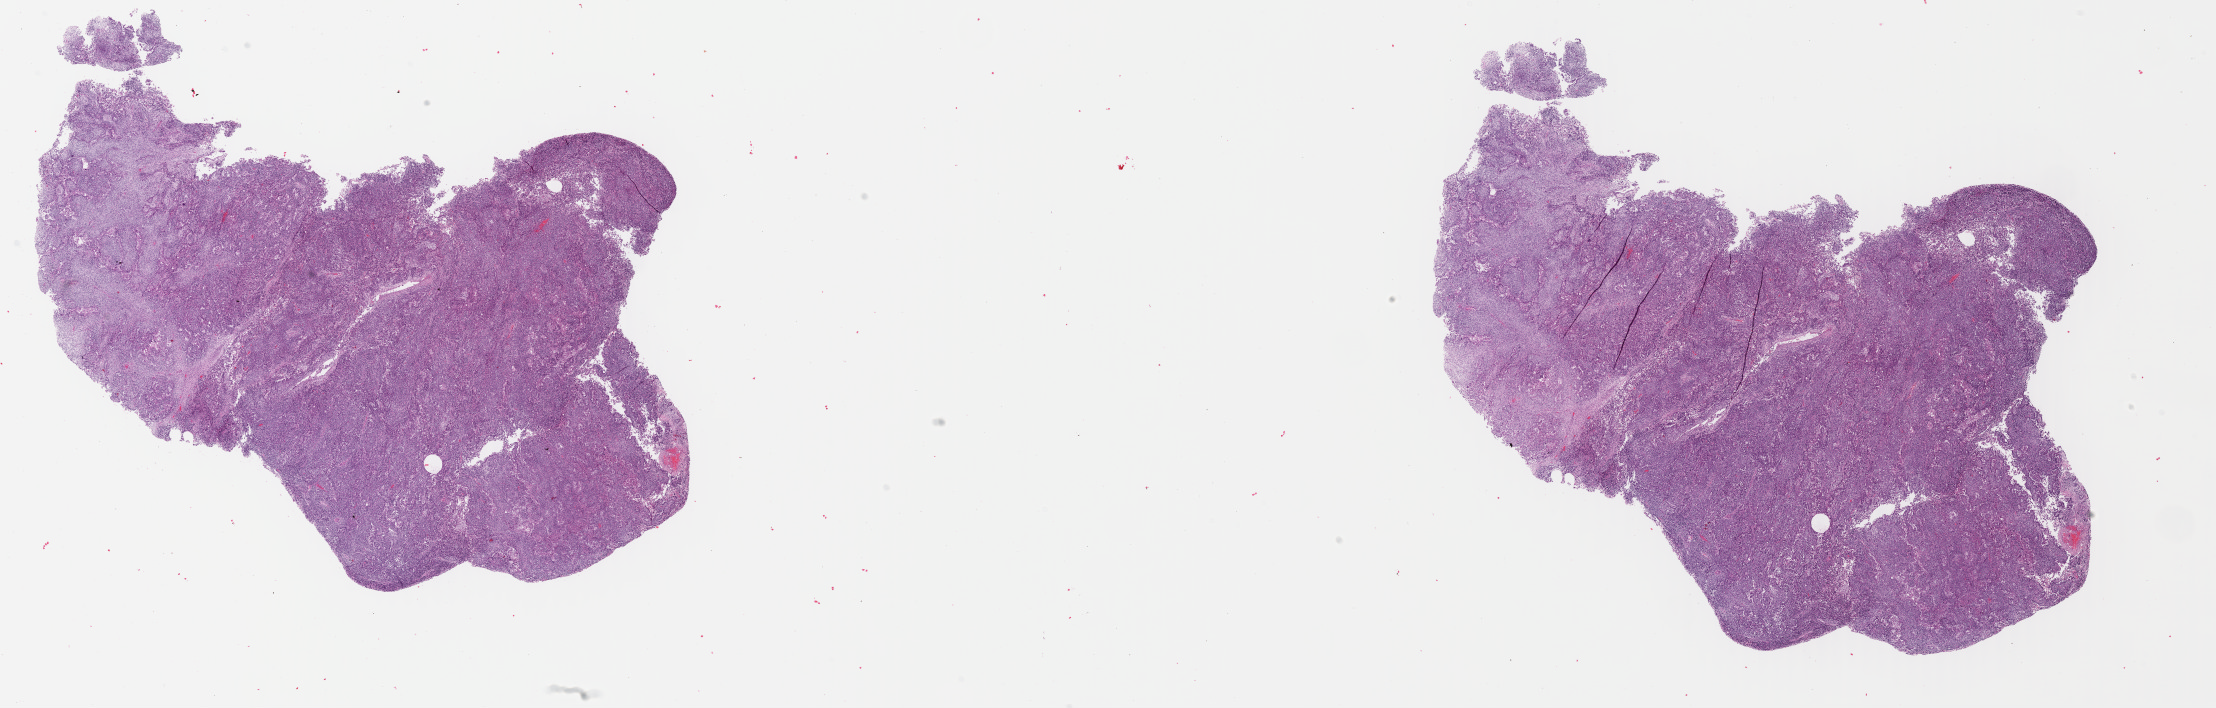
Digitized H&E-stained tissue section (whole slide) — shown as a low-resolution overview of the whole scanned area (about 34.8 x 11.1 mm); formalin-fixed paraffin-embedded (FFPE) diagnostic section; uterus, primary tumour sample. Patient: female, age at initial diagnosis 65 years.
Diagnosis: Mullerian mixed tumor. FIGO stage: IA.